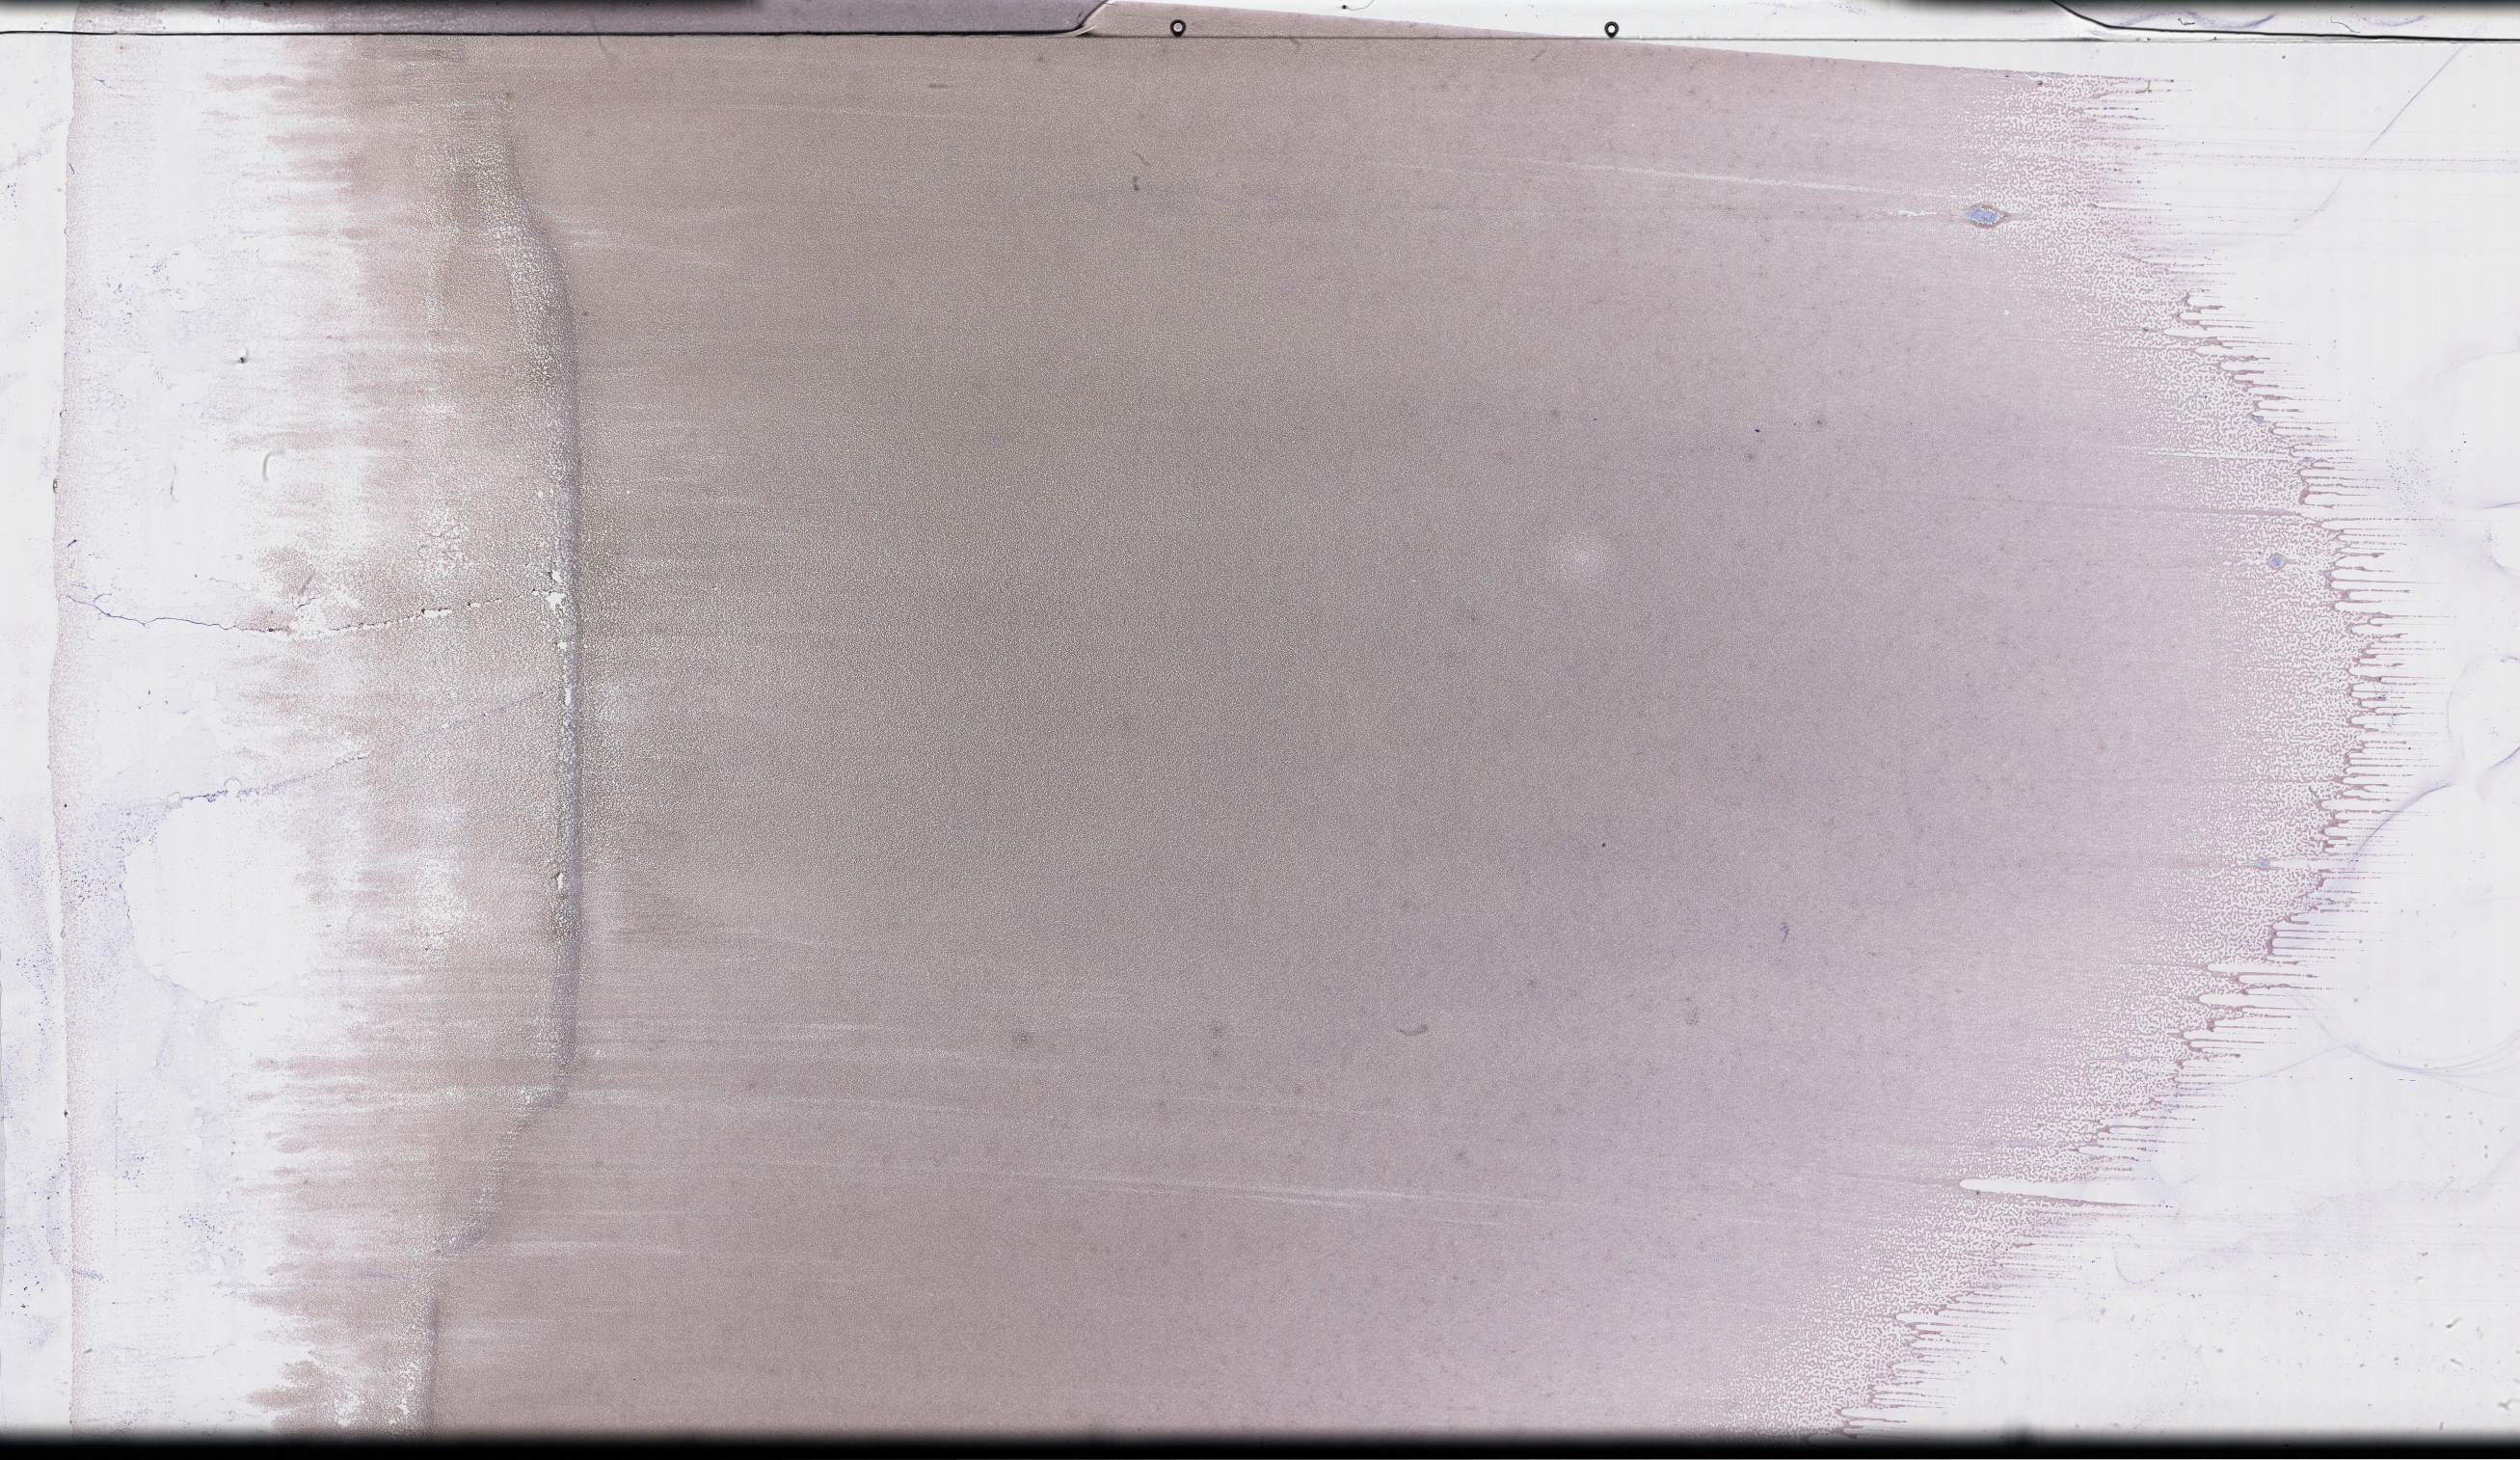
Wright-Giemsa-stained whole blood smear, whole-slide image, low-resolution overview of the scanned area, about 42.2 x 24.5 mm, EDTA-anticoagulated smear. Patient: female.
From a patient with: Plasma Cell Myeloma.